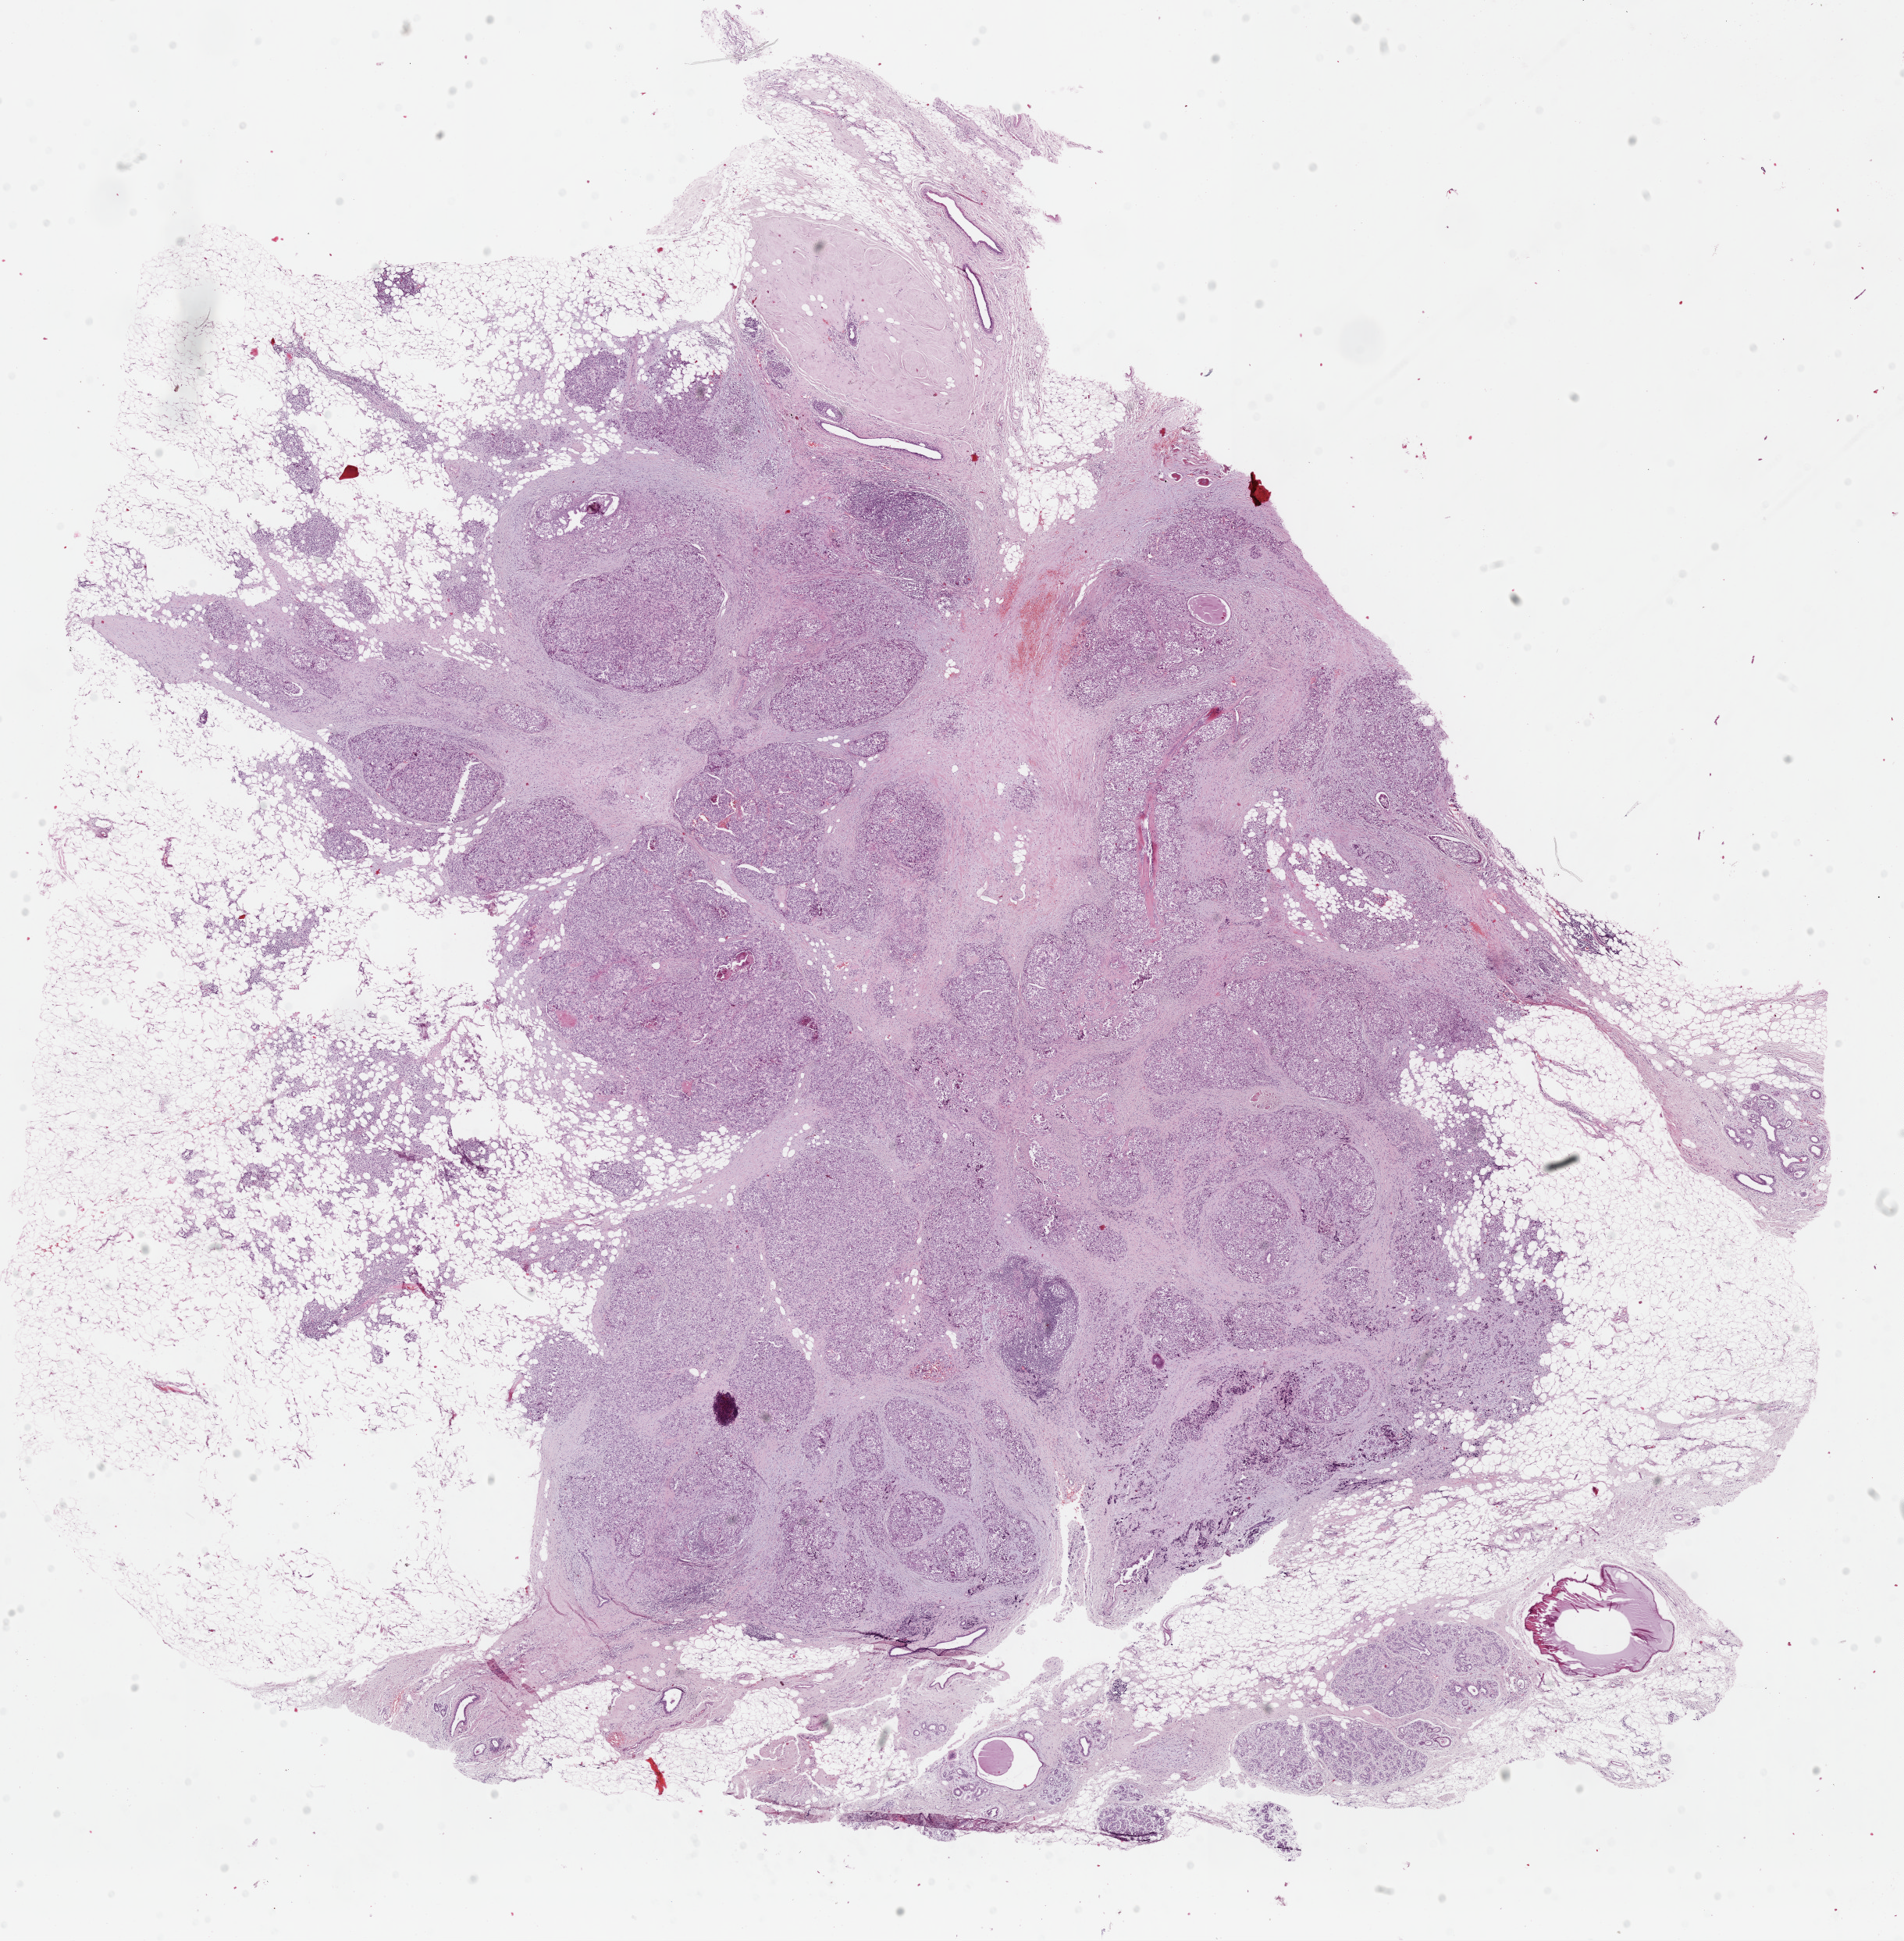
Digitized H&E tissue section (whole slide) — shown as a low-resolution overview of the whole scanned area (about 19.3 x 19.6 mm, from a 40x scan); FFPE section; breast, primary tumour sample. Female, age 45 years at initial diagnosis.
• diagnosis: Infiltrating duct carcinoma, NOS
• AJCC pathologic stage: IIA (7th edition)
• laterality: left